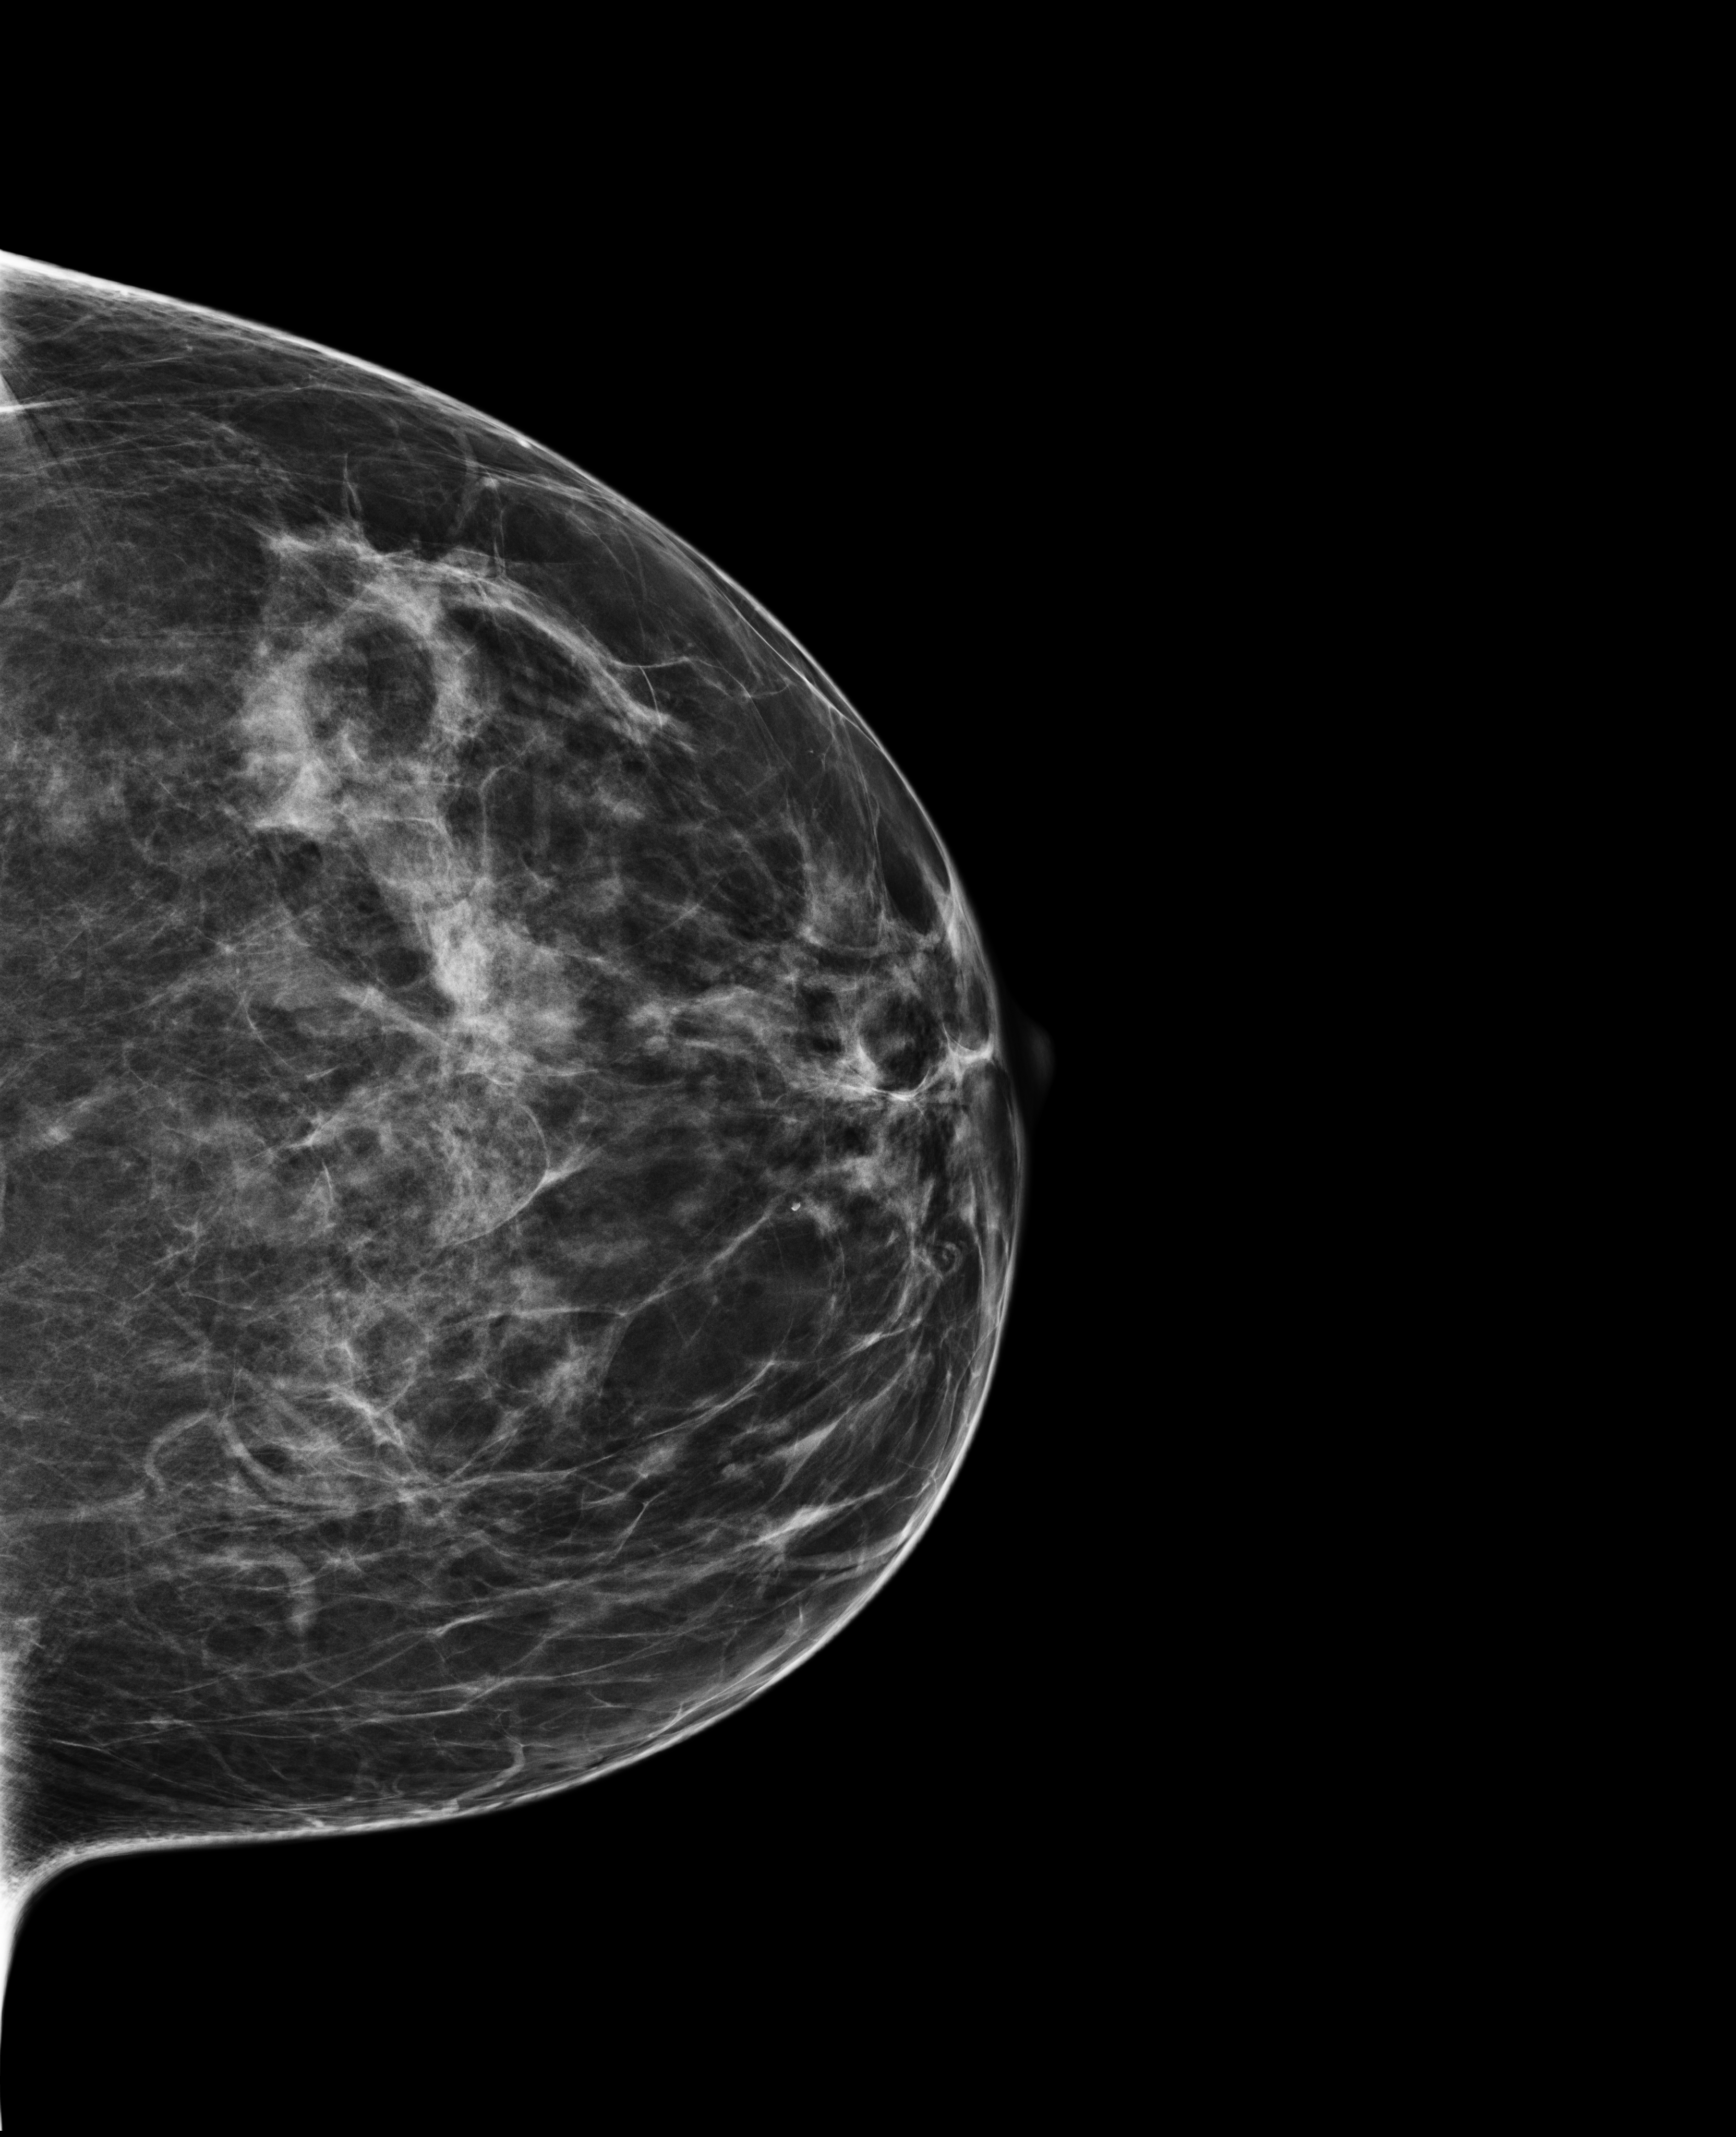
Screening examination, compressed breast thickness 73 mm, system: Selenia Dimensions. Patient aged 48 years (female).
Image type: full-field digital mammogram. Breast: left. Projection: CC view.